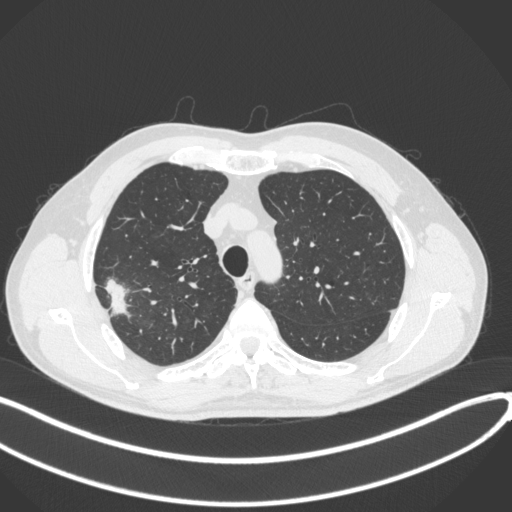
Chest CT, one axial slice. Position 323 of 381 along the scan axis. Reconstruction kernel B31f. 120 kVp. Lung window (W 1500 / L -600 HU). 512 × 512 image matrix, field of view 400 × 400 mm. Male patient, age 62 years. Case-level facts recorded for this patient, not image findings: clinical TNM (as recorded): T1c N0 M0; histopathological grade: G2-3.
Structures marked on this image (bounding box drawn by a radiologist):
- lung tumour (recorded histology: adenocarcinoma): box from (x=101, y=275) to (x=131, y=318) px